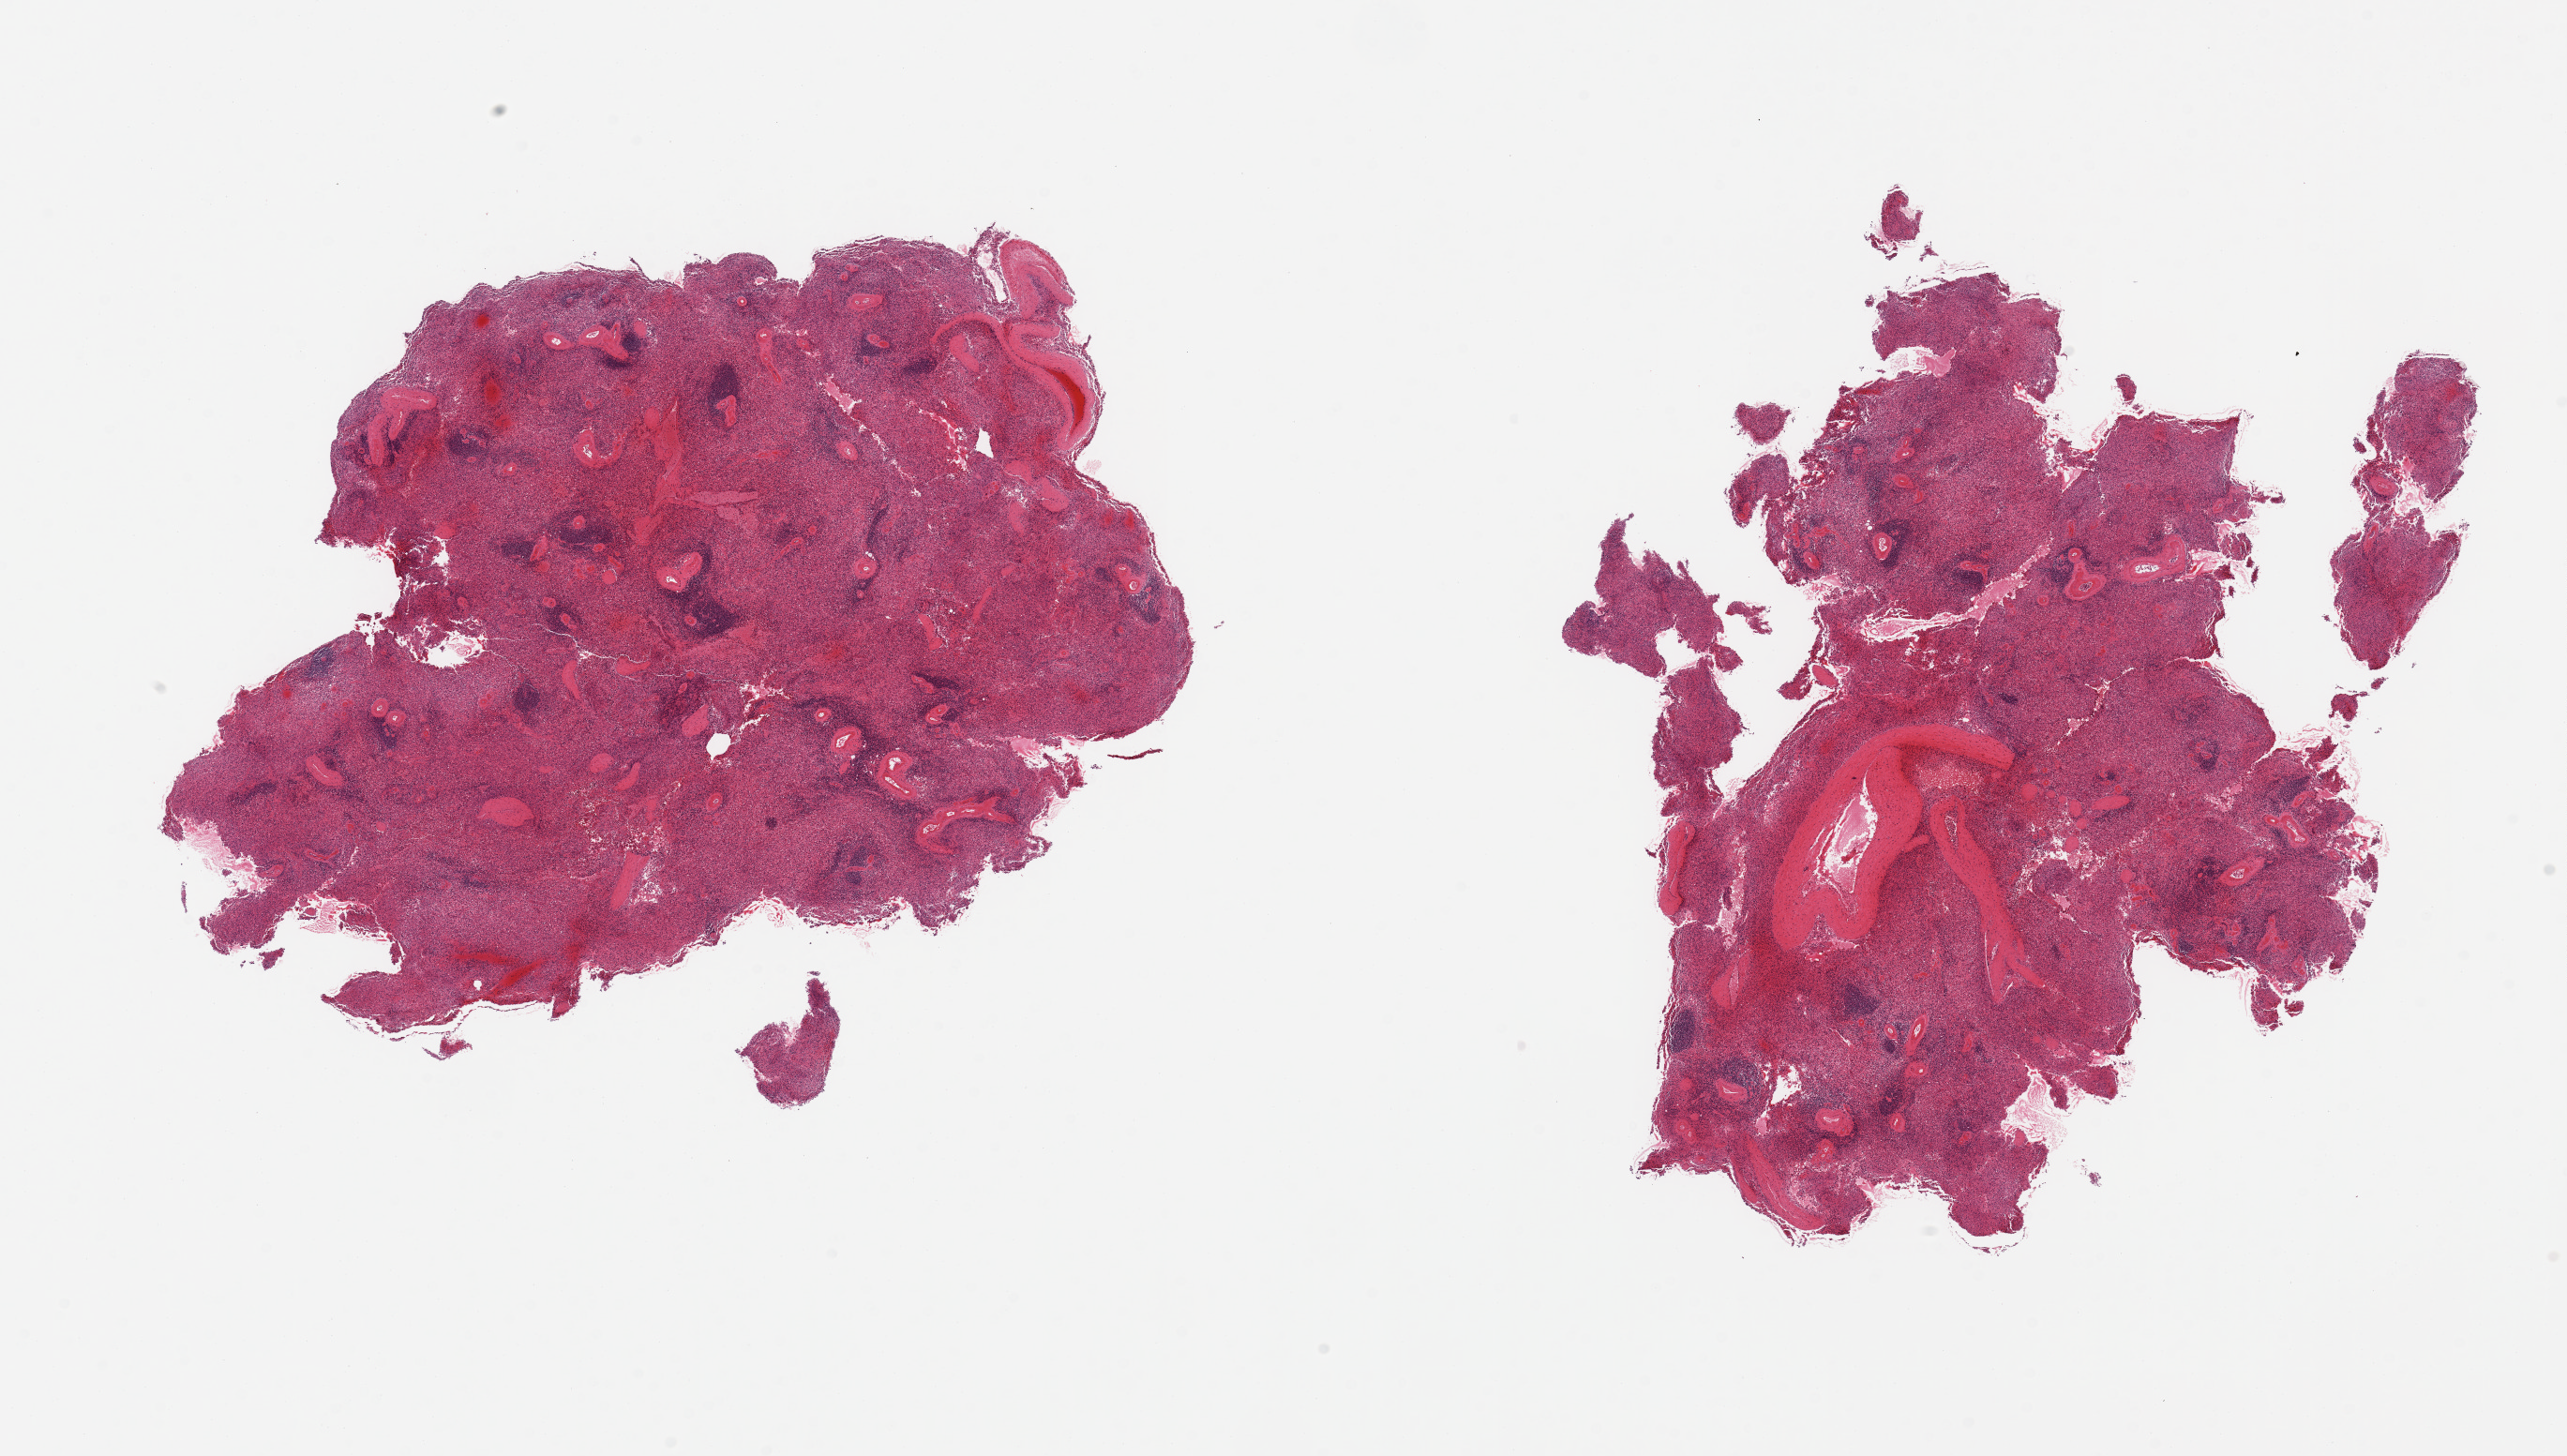
H&E whole-slide image, brightfield — low-resolution overview of the scanned area, about 21.7 x 12.3 mm (slide scanned at 20x). PAXgene-fixed paraffin-embedded (PFPE) section. Sampled site (target tissue): spleen. Donor tissue sample. Female donor.
Review note (as recorded): 2 fragmented pieces; moderate congestion.